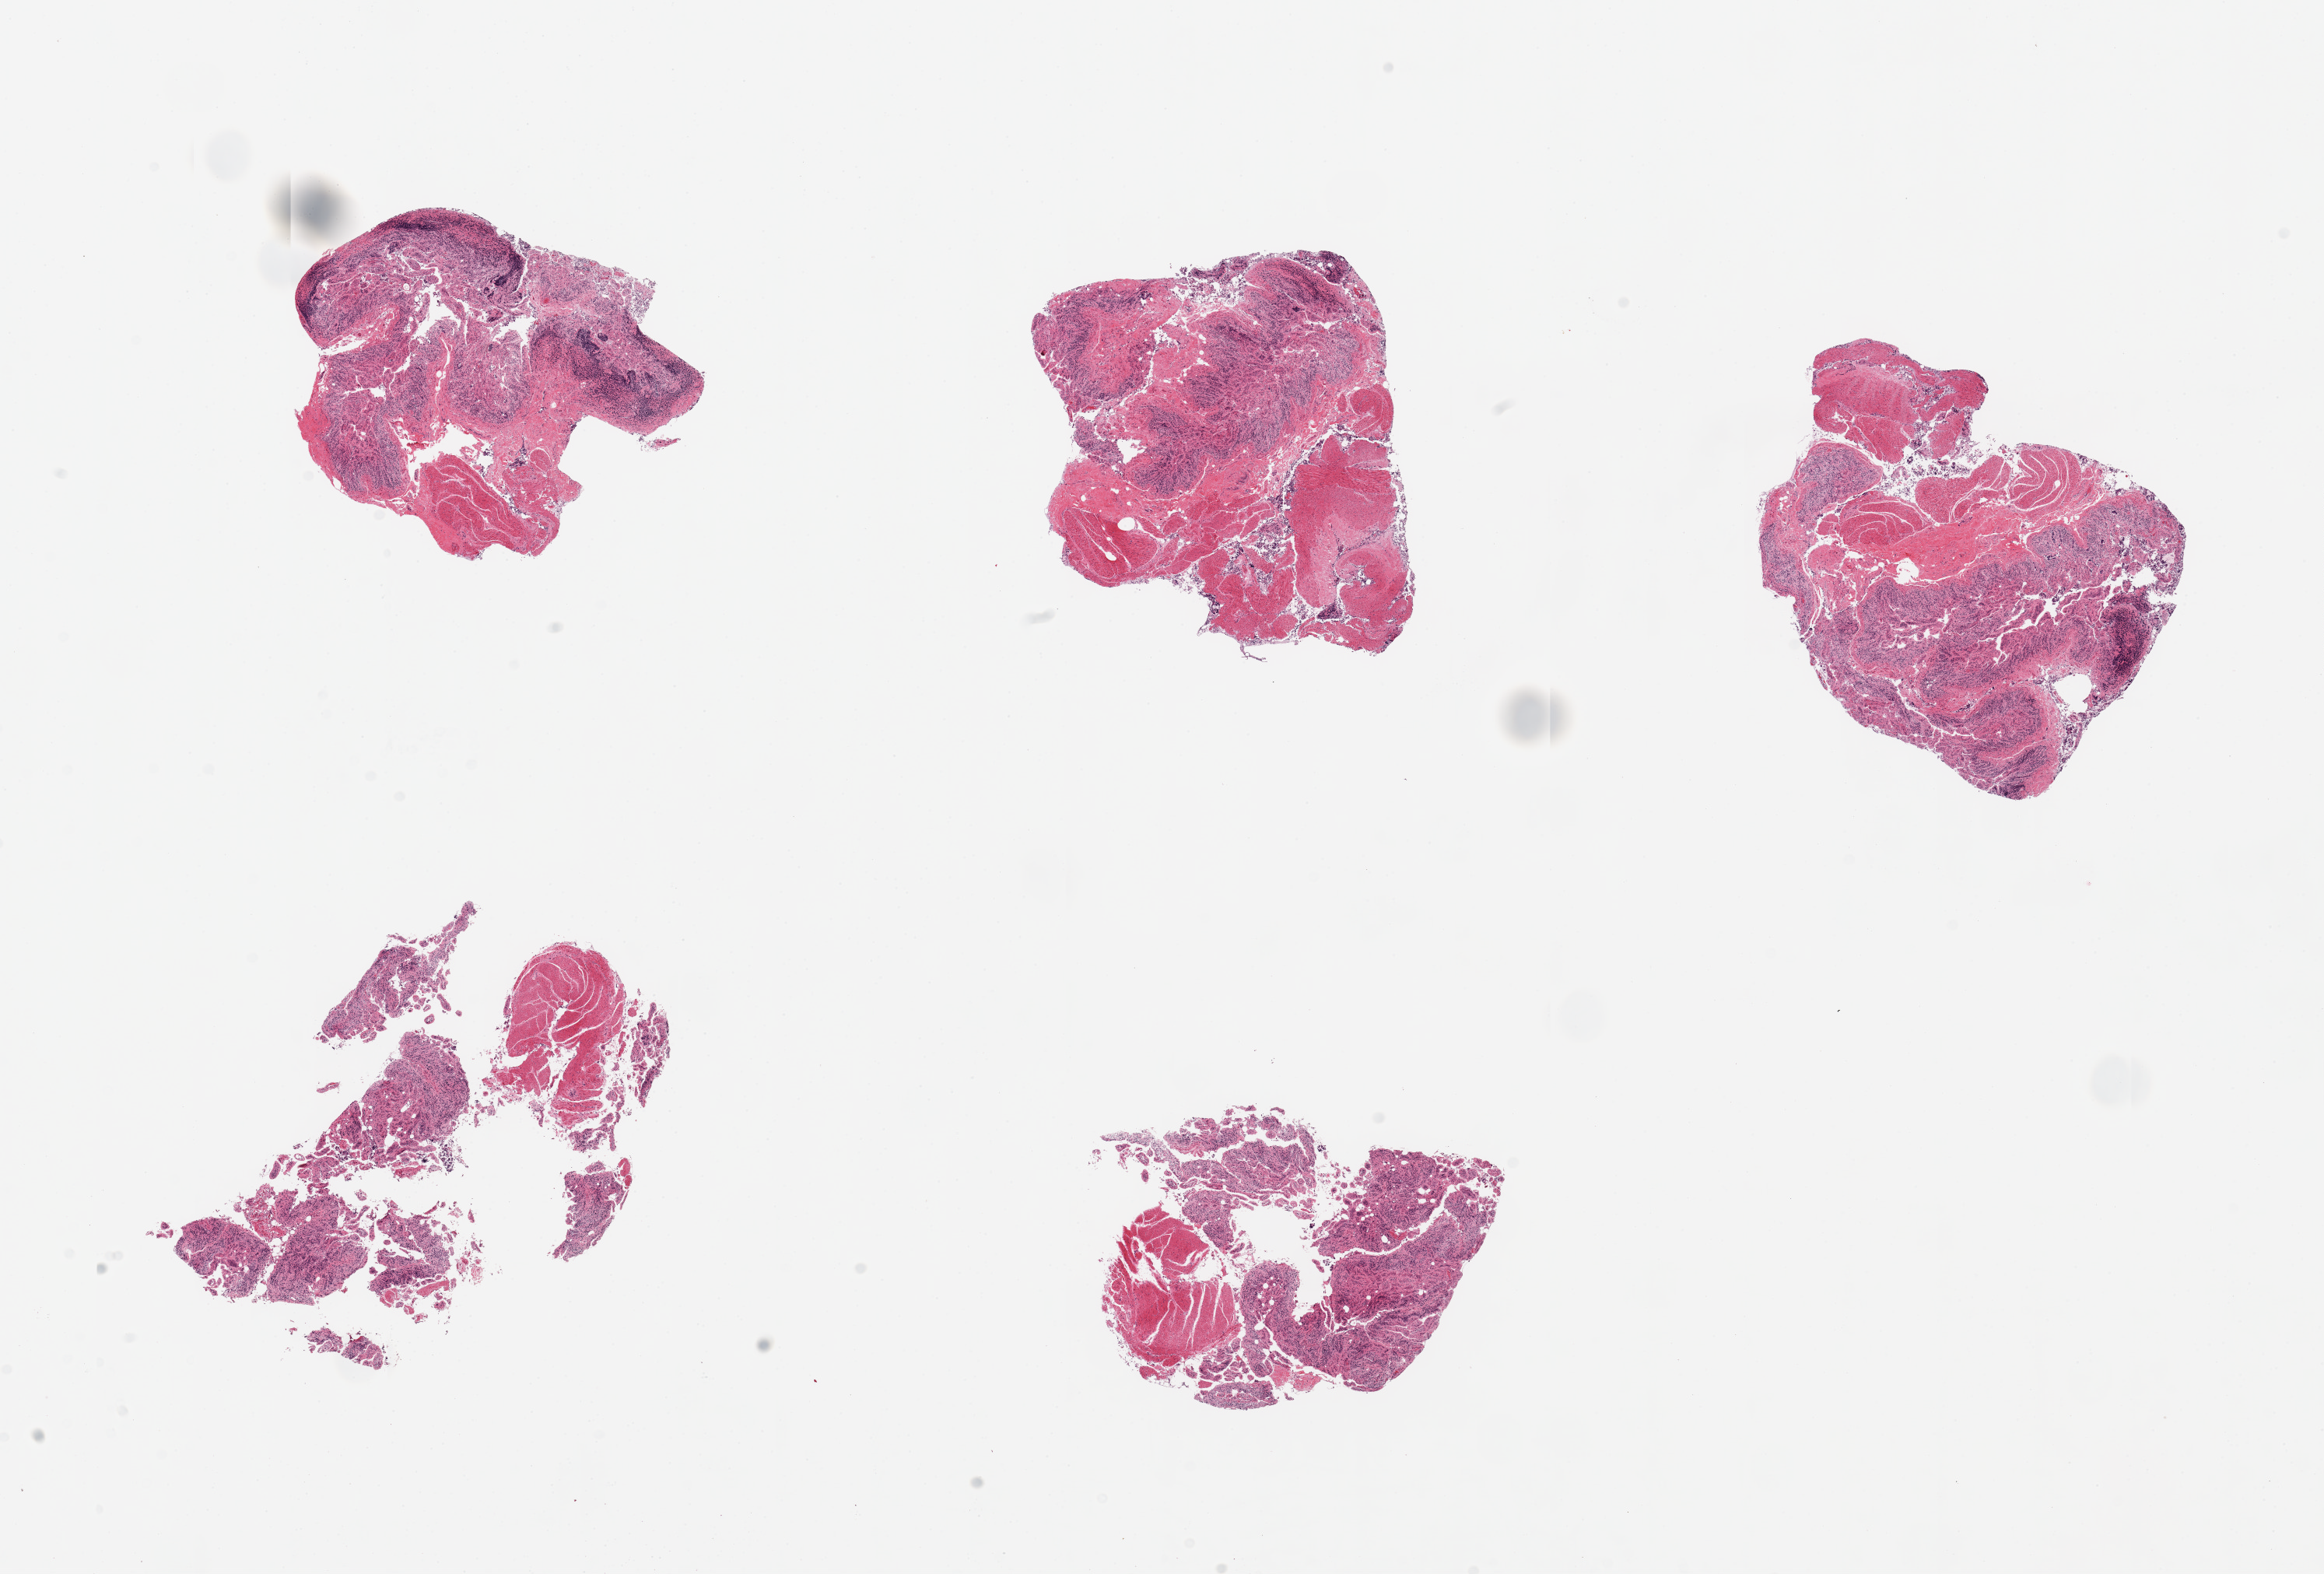
H&E whole-slide image — whole scanned area (about 23.6 x 16.0 mm) shown as a low-resolution overview. PAXgene-fixed paraffin-embedded (PFPE) section. Sampled site (target tissue): ileum. Donor tissue sample. Male donor.
Reviewer comment on this tissue sample: 5 pieces; fragments of muscularis (not target) and autolyzed mucosa with no significant lymphoid tissue.